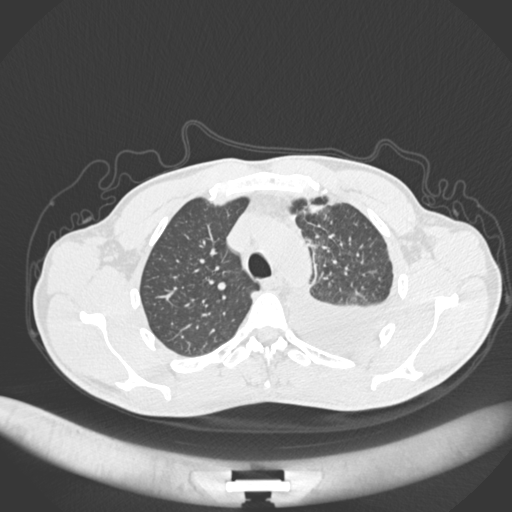
Chest CT, one axial slice; position 171 of 244 along the scan axis; reconstruction kernel B30f; lung window (W 1500 / L -600 HU); 512 × 512 image matrix, field of view 400 × 400 mm. Patient: male, 49 years. Case-level facts recorded for this patient, not image findings: clinical TNM (as recorded): T1c N1 M1.
Structures marked on this image (rectangle marked by the reading radiologist):
- lung tumour (recorded histology: adenocarcinoma): bounding box <300,200,327,216> (left, top, right, bottom; pixels)